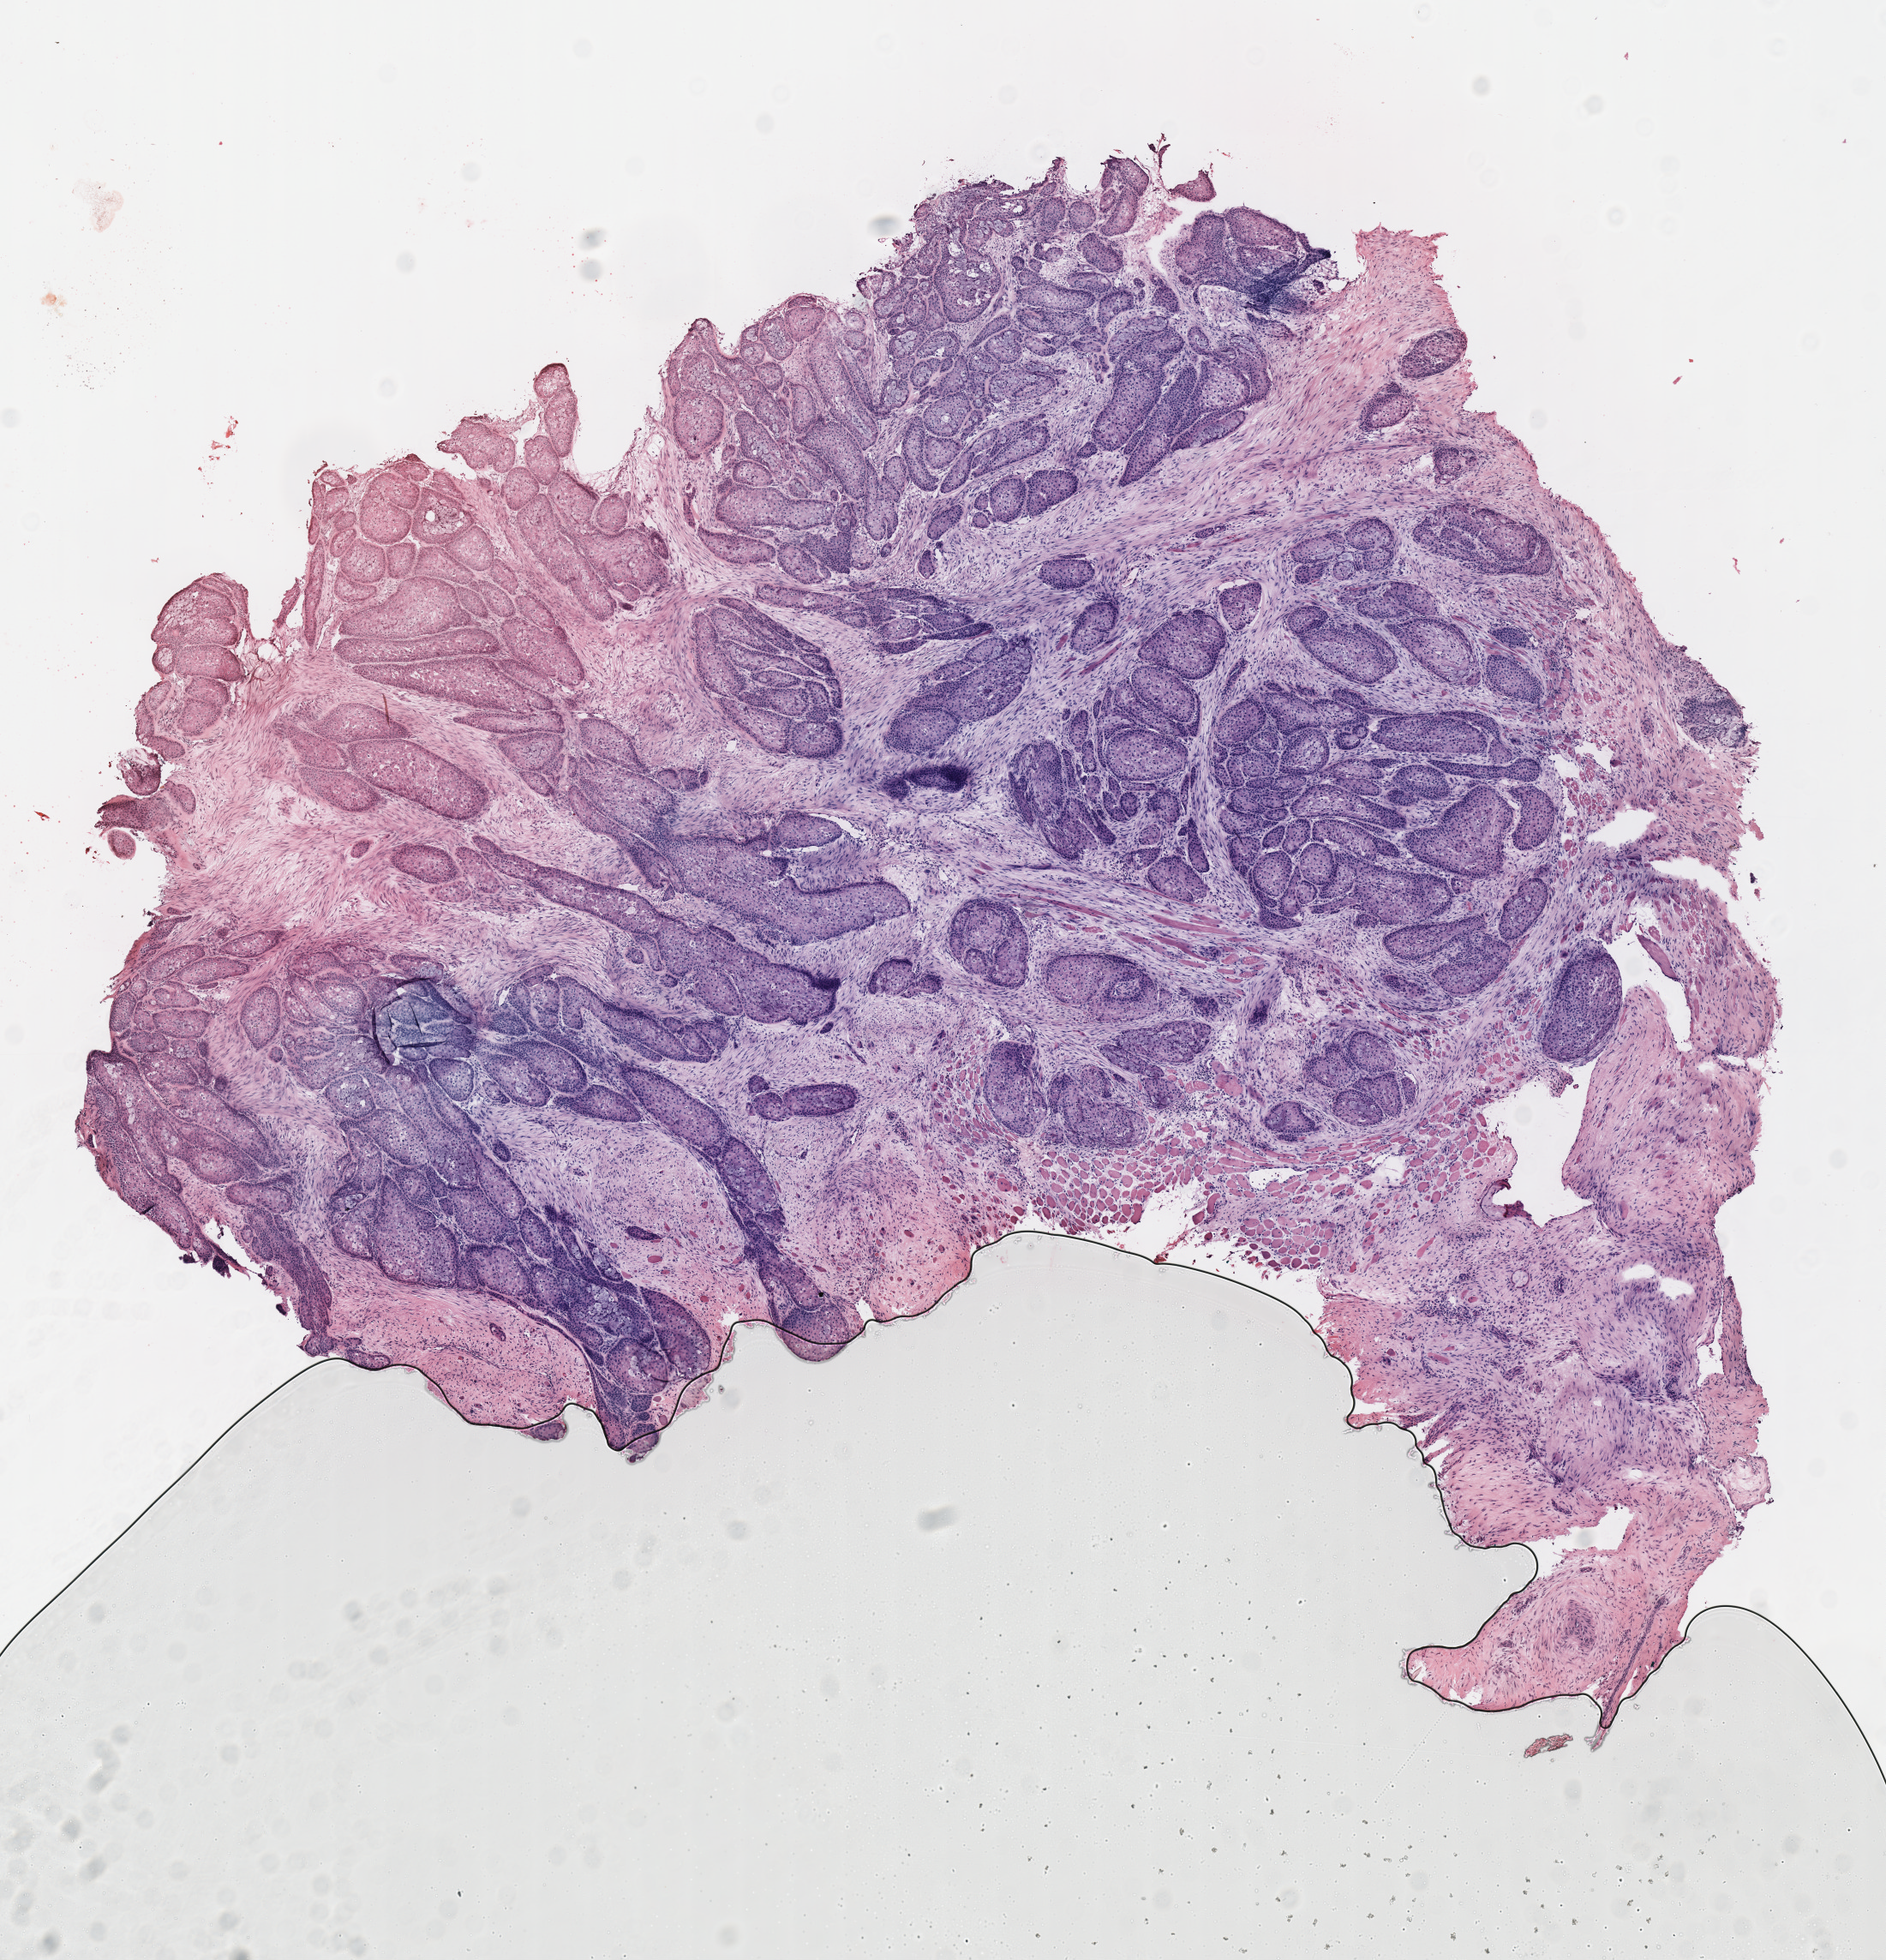
Whole-slide histology image, H&E — a low-resolution overview of the entire scanned area, about 8.7 x 9.0 mm (acquisition: 40x scan); frozen section from the top of the tissue portion; head and neck, primary tumour sample. Female patient; age at initial diagnosis 60 years. Histologic grade: G1 (well differentiated). Pathologist review of this section (percent, as recorded): tumour cells 70%, tumour nuclei 60%, normal cells 0%, stromal cells 30%, necrosis 0%.
AJCC pathologic stage: II (7th edition). Lymph nodes positive (case pathology): 0 of 48 examined. Diagnosis: Squamous cell carcinoma, NOS (cheek mucosa).